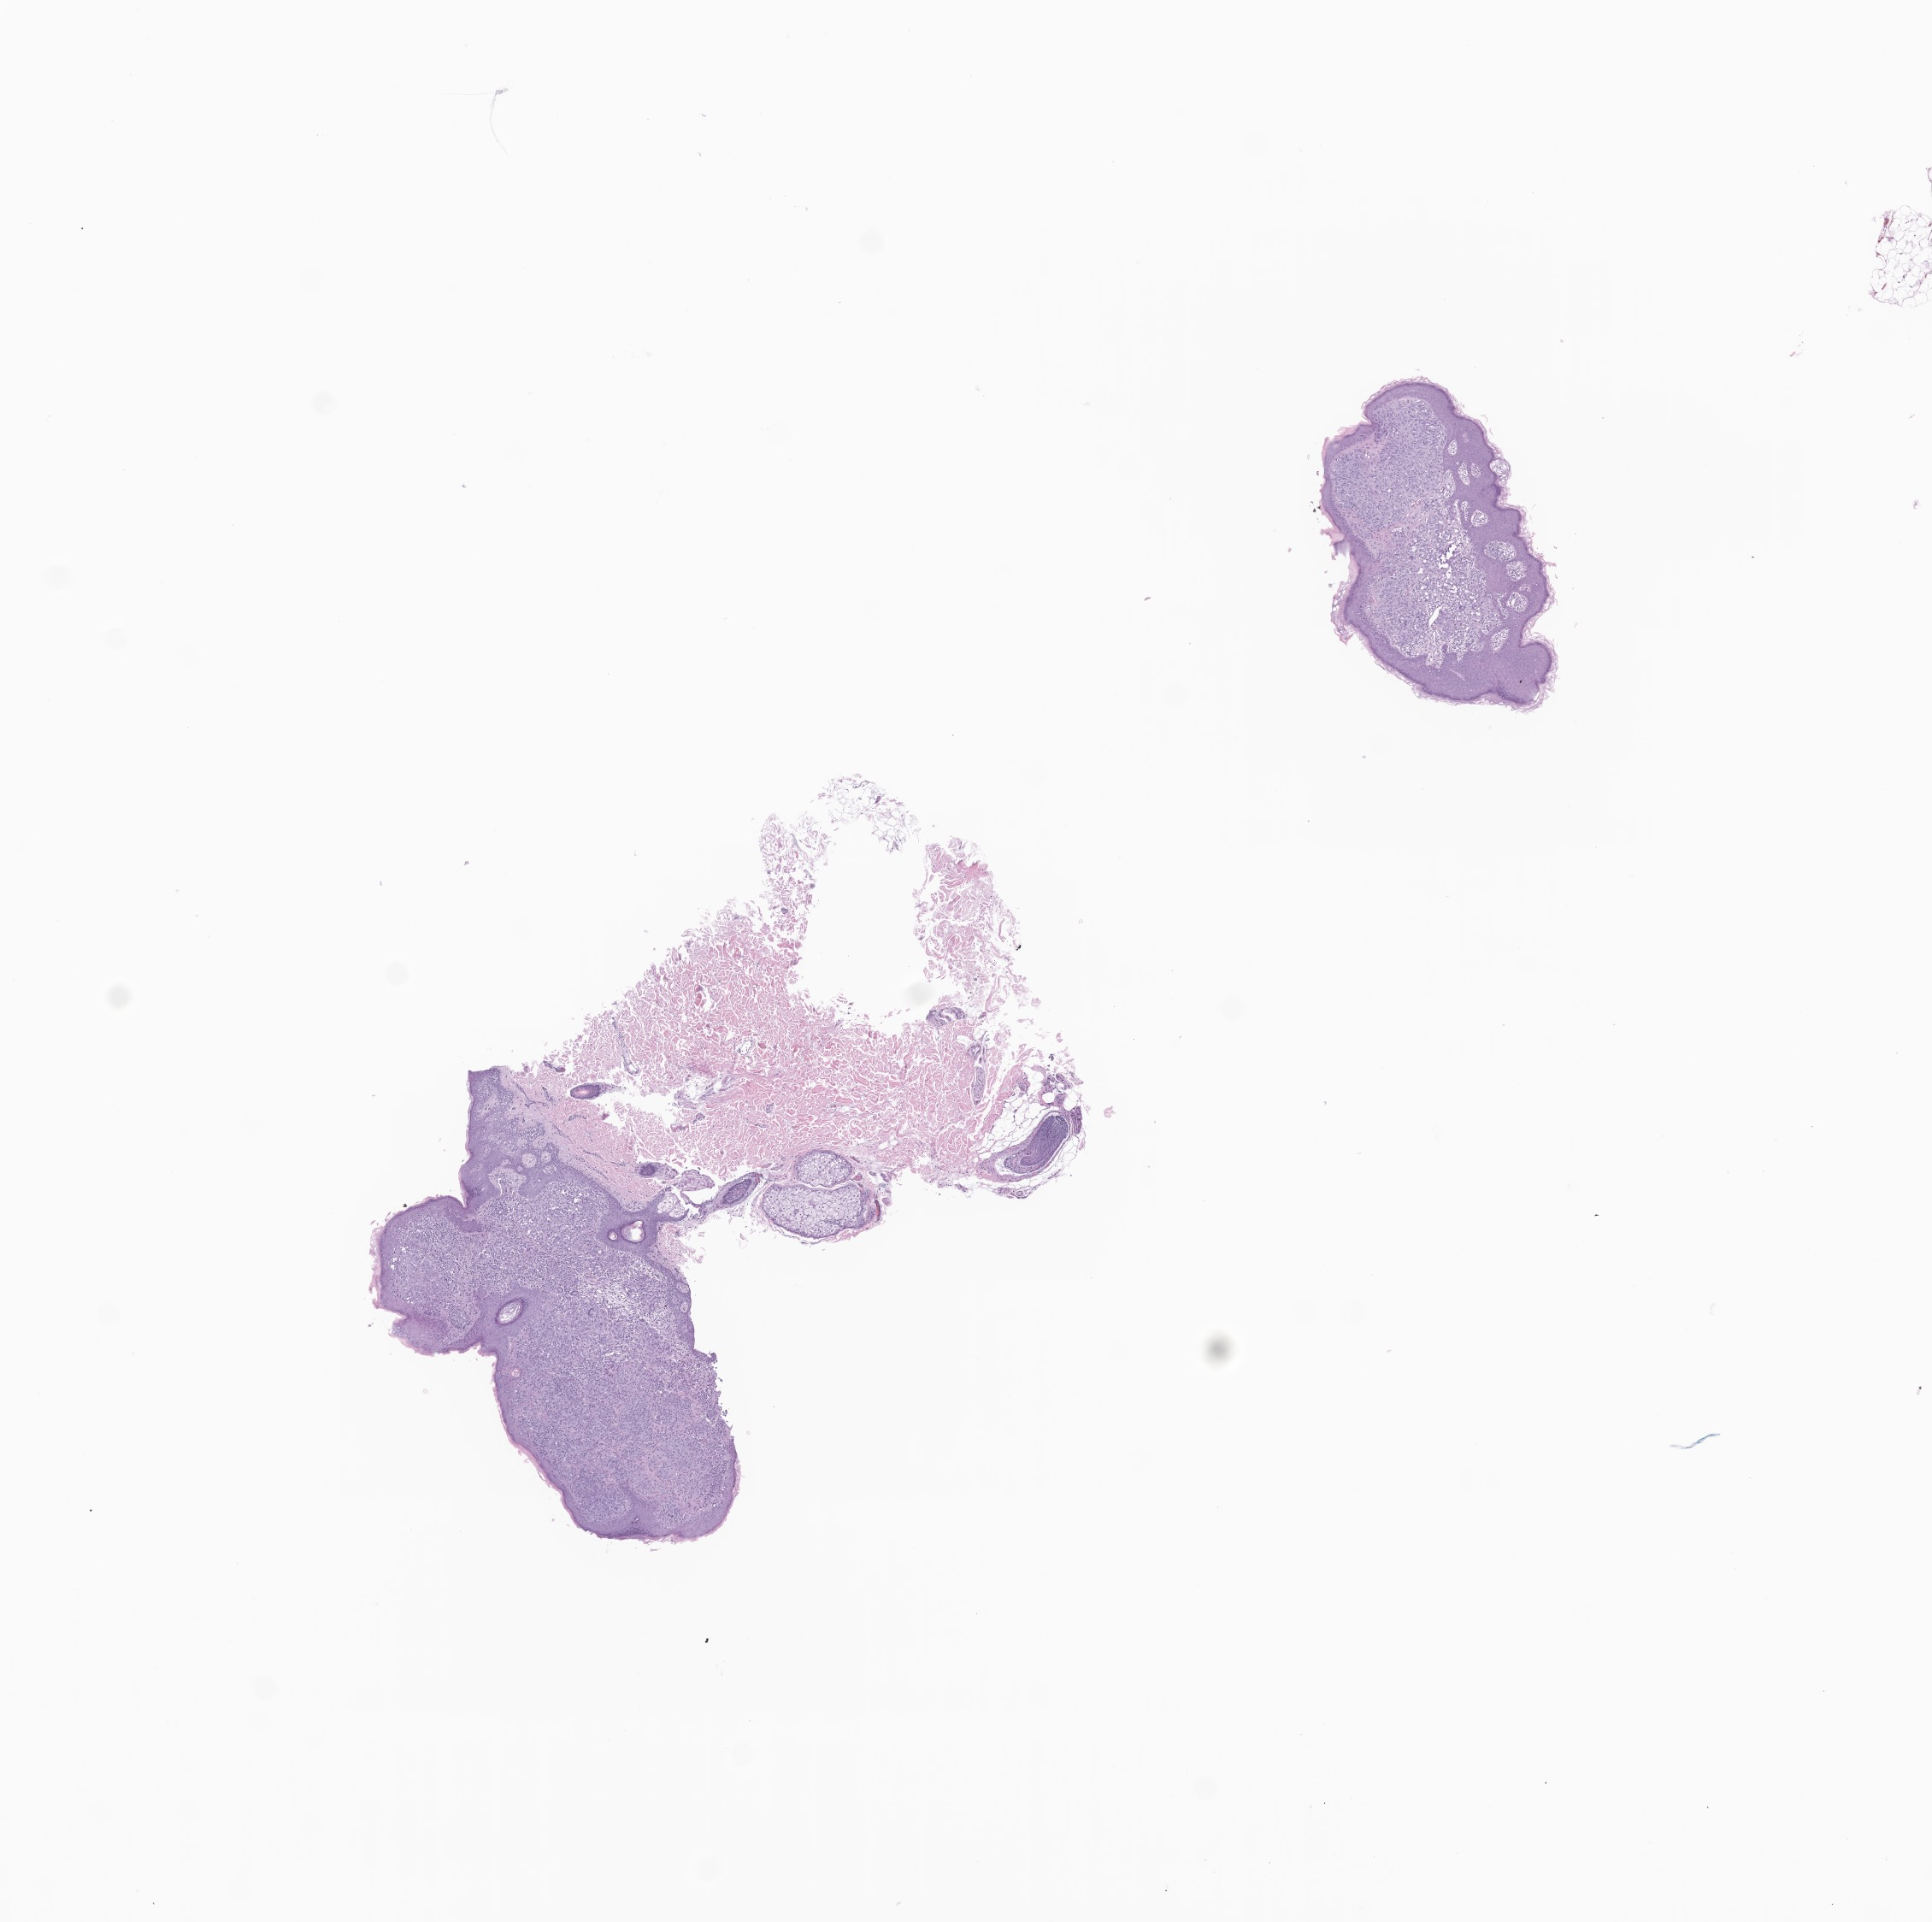
Whole-slide image, hematoxylin and eosin (H&E) stain of tumor tissue from the soft tissues of head and neck, whole scanned area (about 9.5 x 9.5 mm) shown as a low-resolution overview; FFPE section. Patient female; age 156 months (13 years).
* diagnosis: Tumor cells, uncertain whether benign or malignant